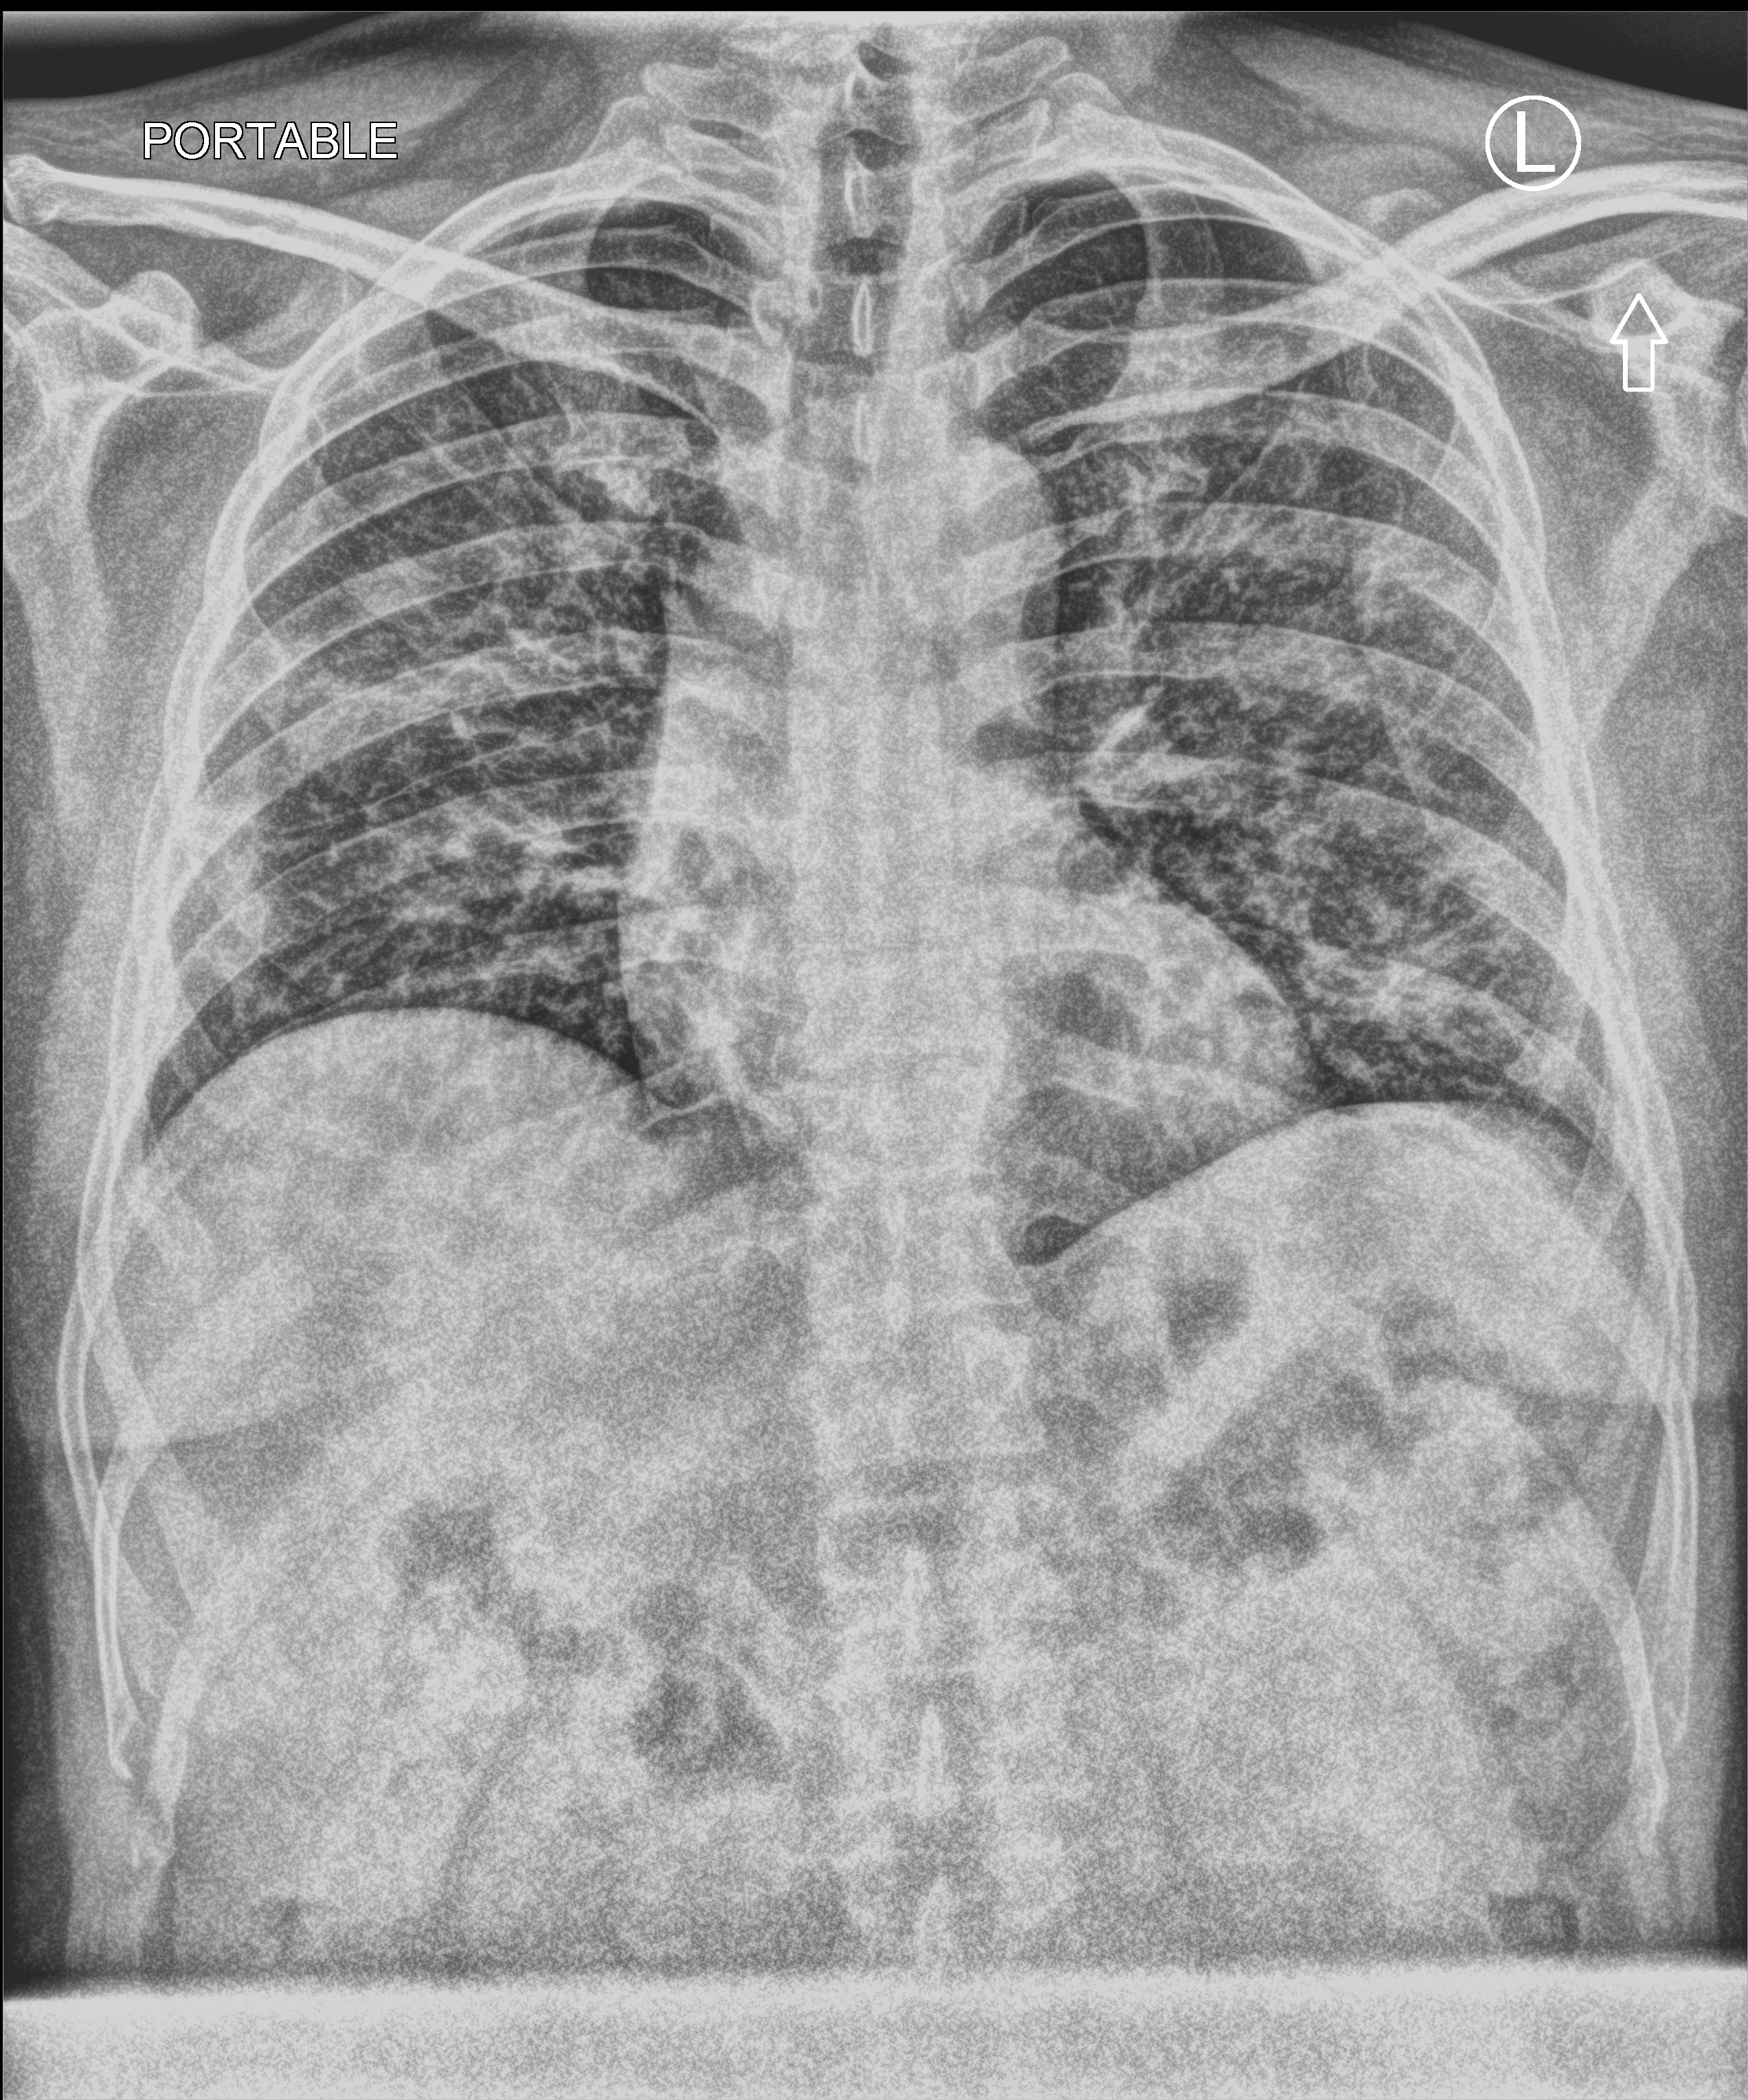
Portable chest radiograph, anteroposterior (AP) projection. Patient hospitalised with COVID-19; male, aged 18–59 years.
Admission-level facts for this patient (not findings on this image; timing relative to this image not recorded): diabetes (admission record): no.